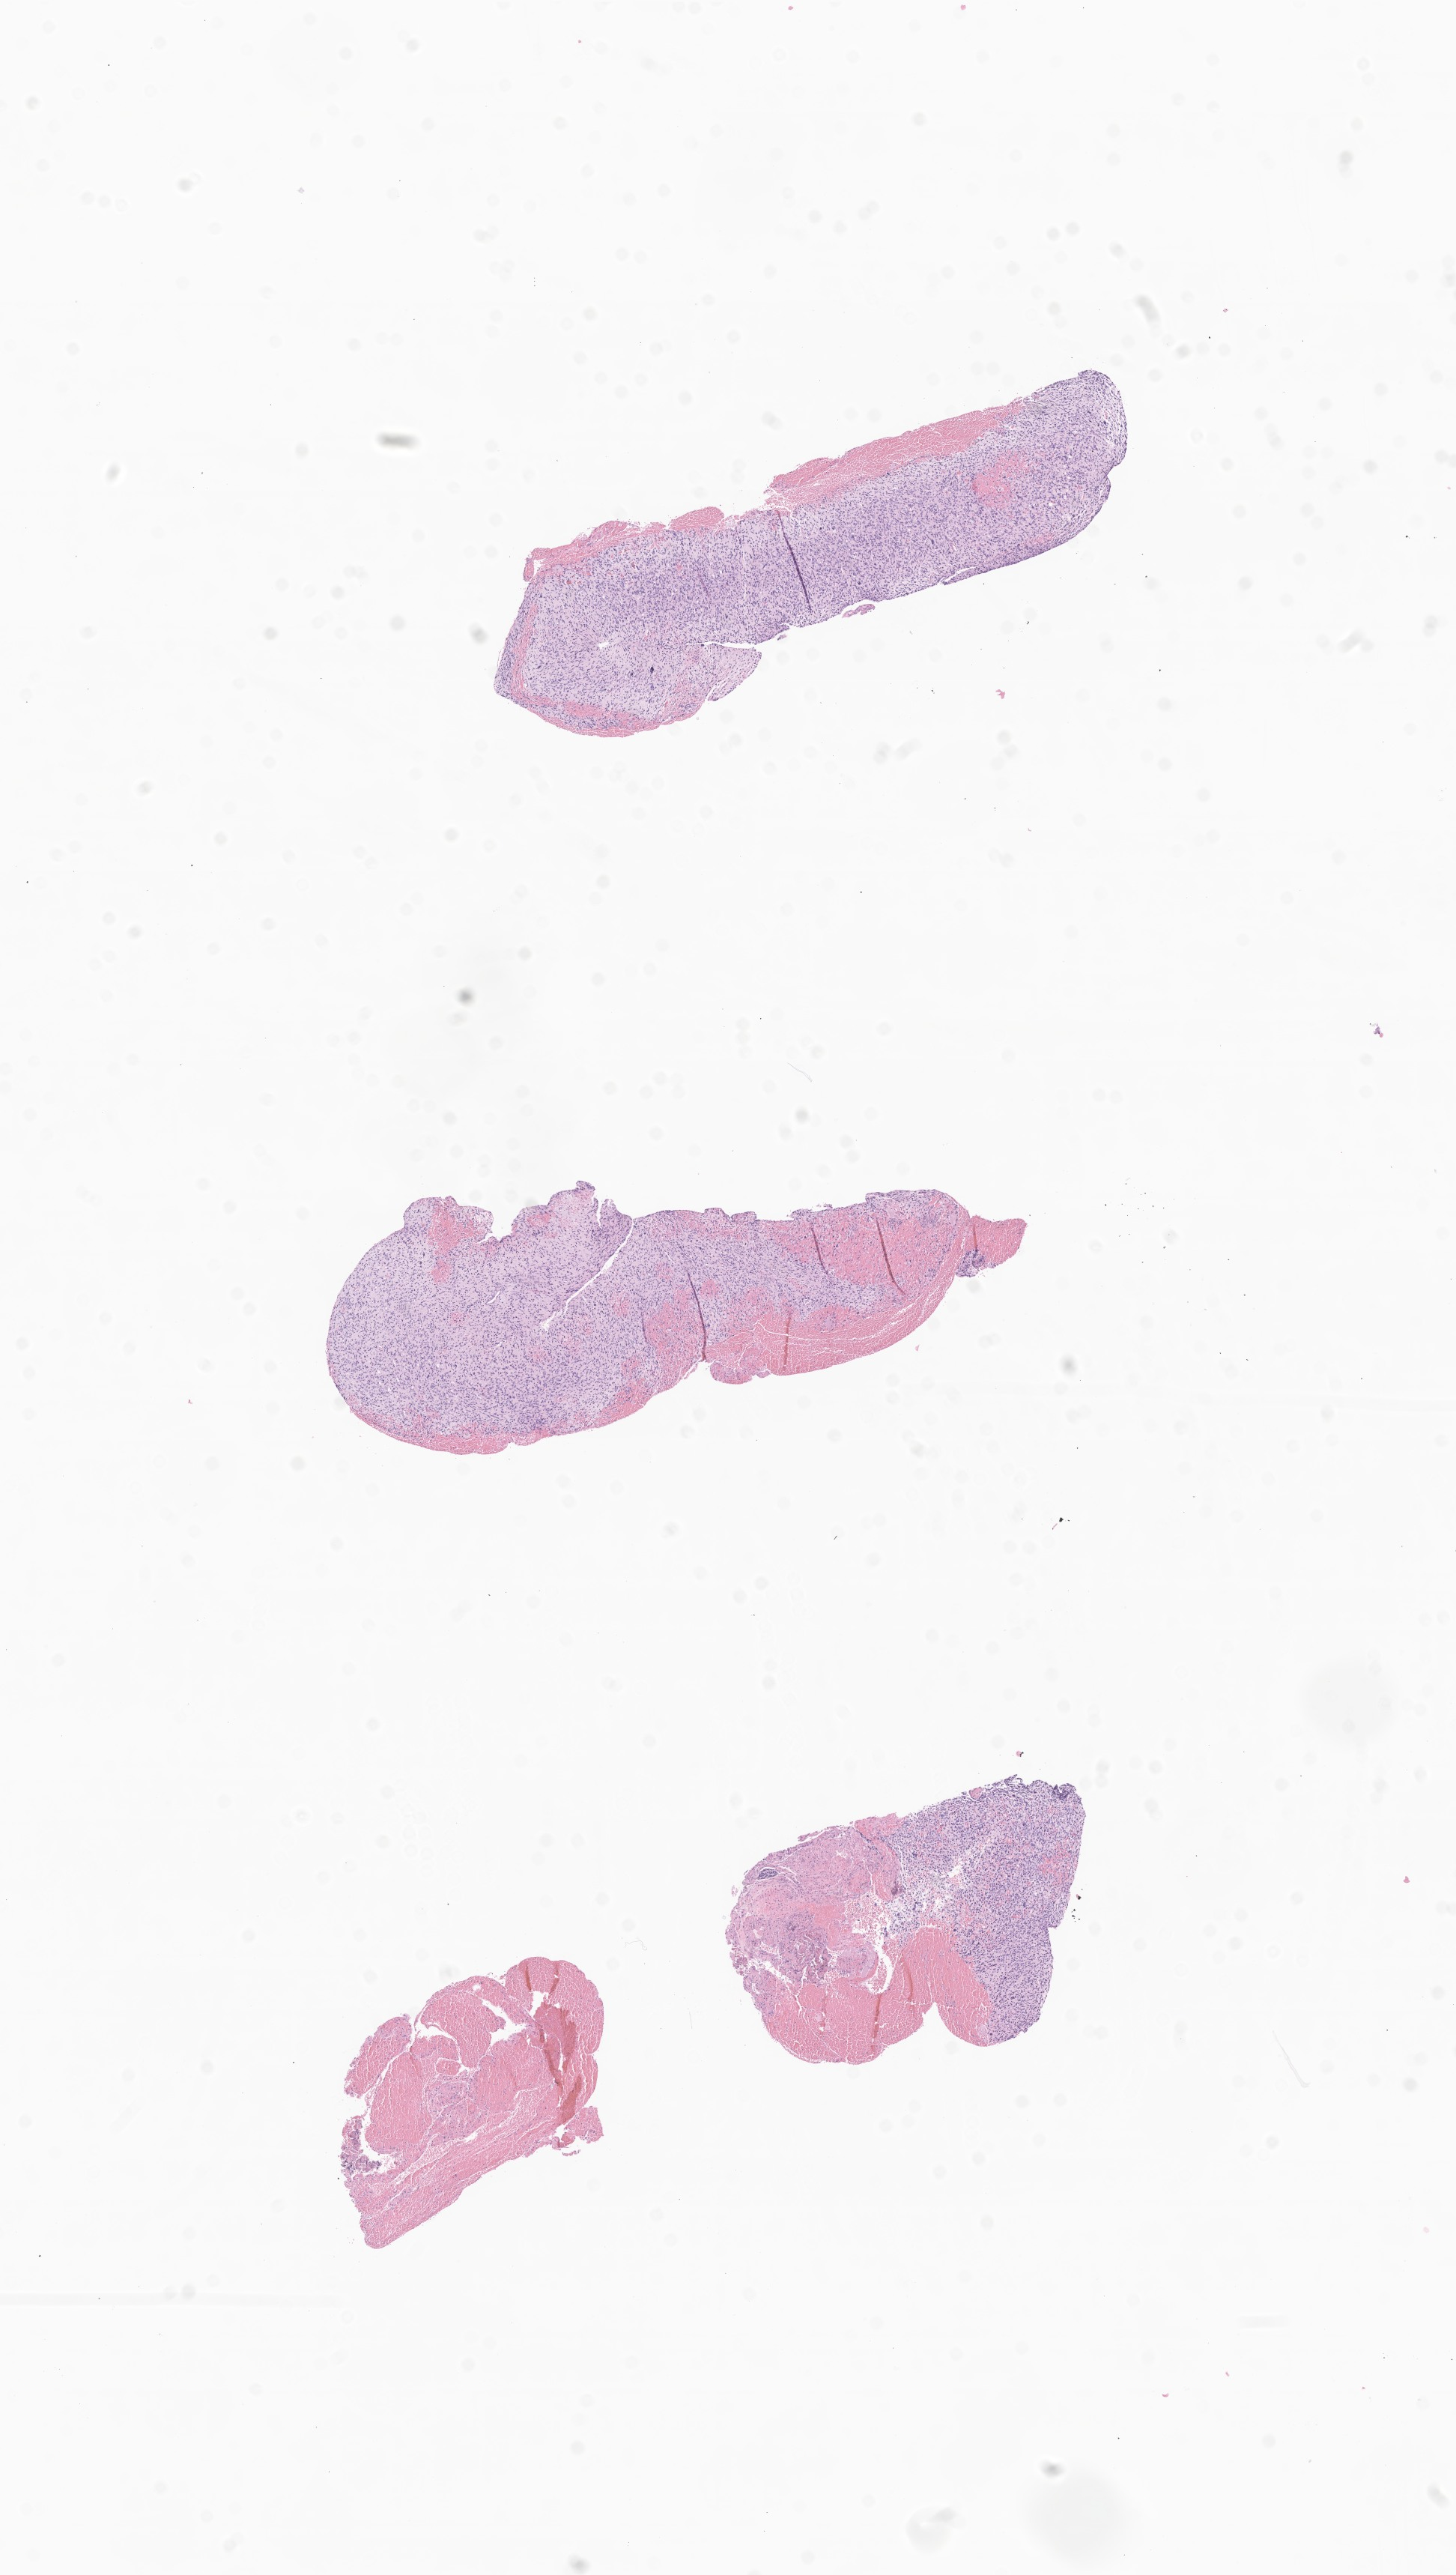
Digitized haematoxylin and eosin-stained section of tumor tissue from the cerebrum — shown as a low-resolution overview of the whole scanned area (about 8.2 x 14.5 mm). FFPE section. Male patient, age 66 months (5 years 6 months).
Recorded diagnosis: Glioma, malignant.